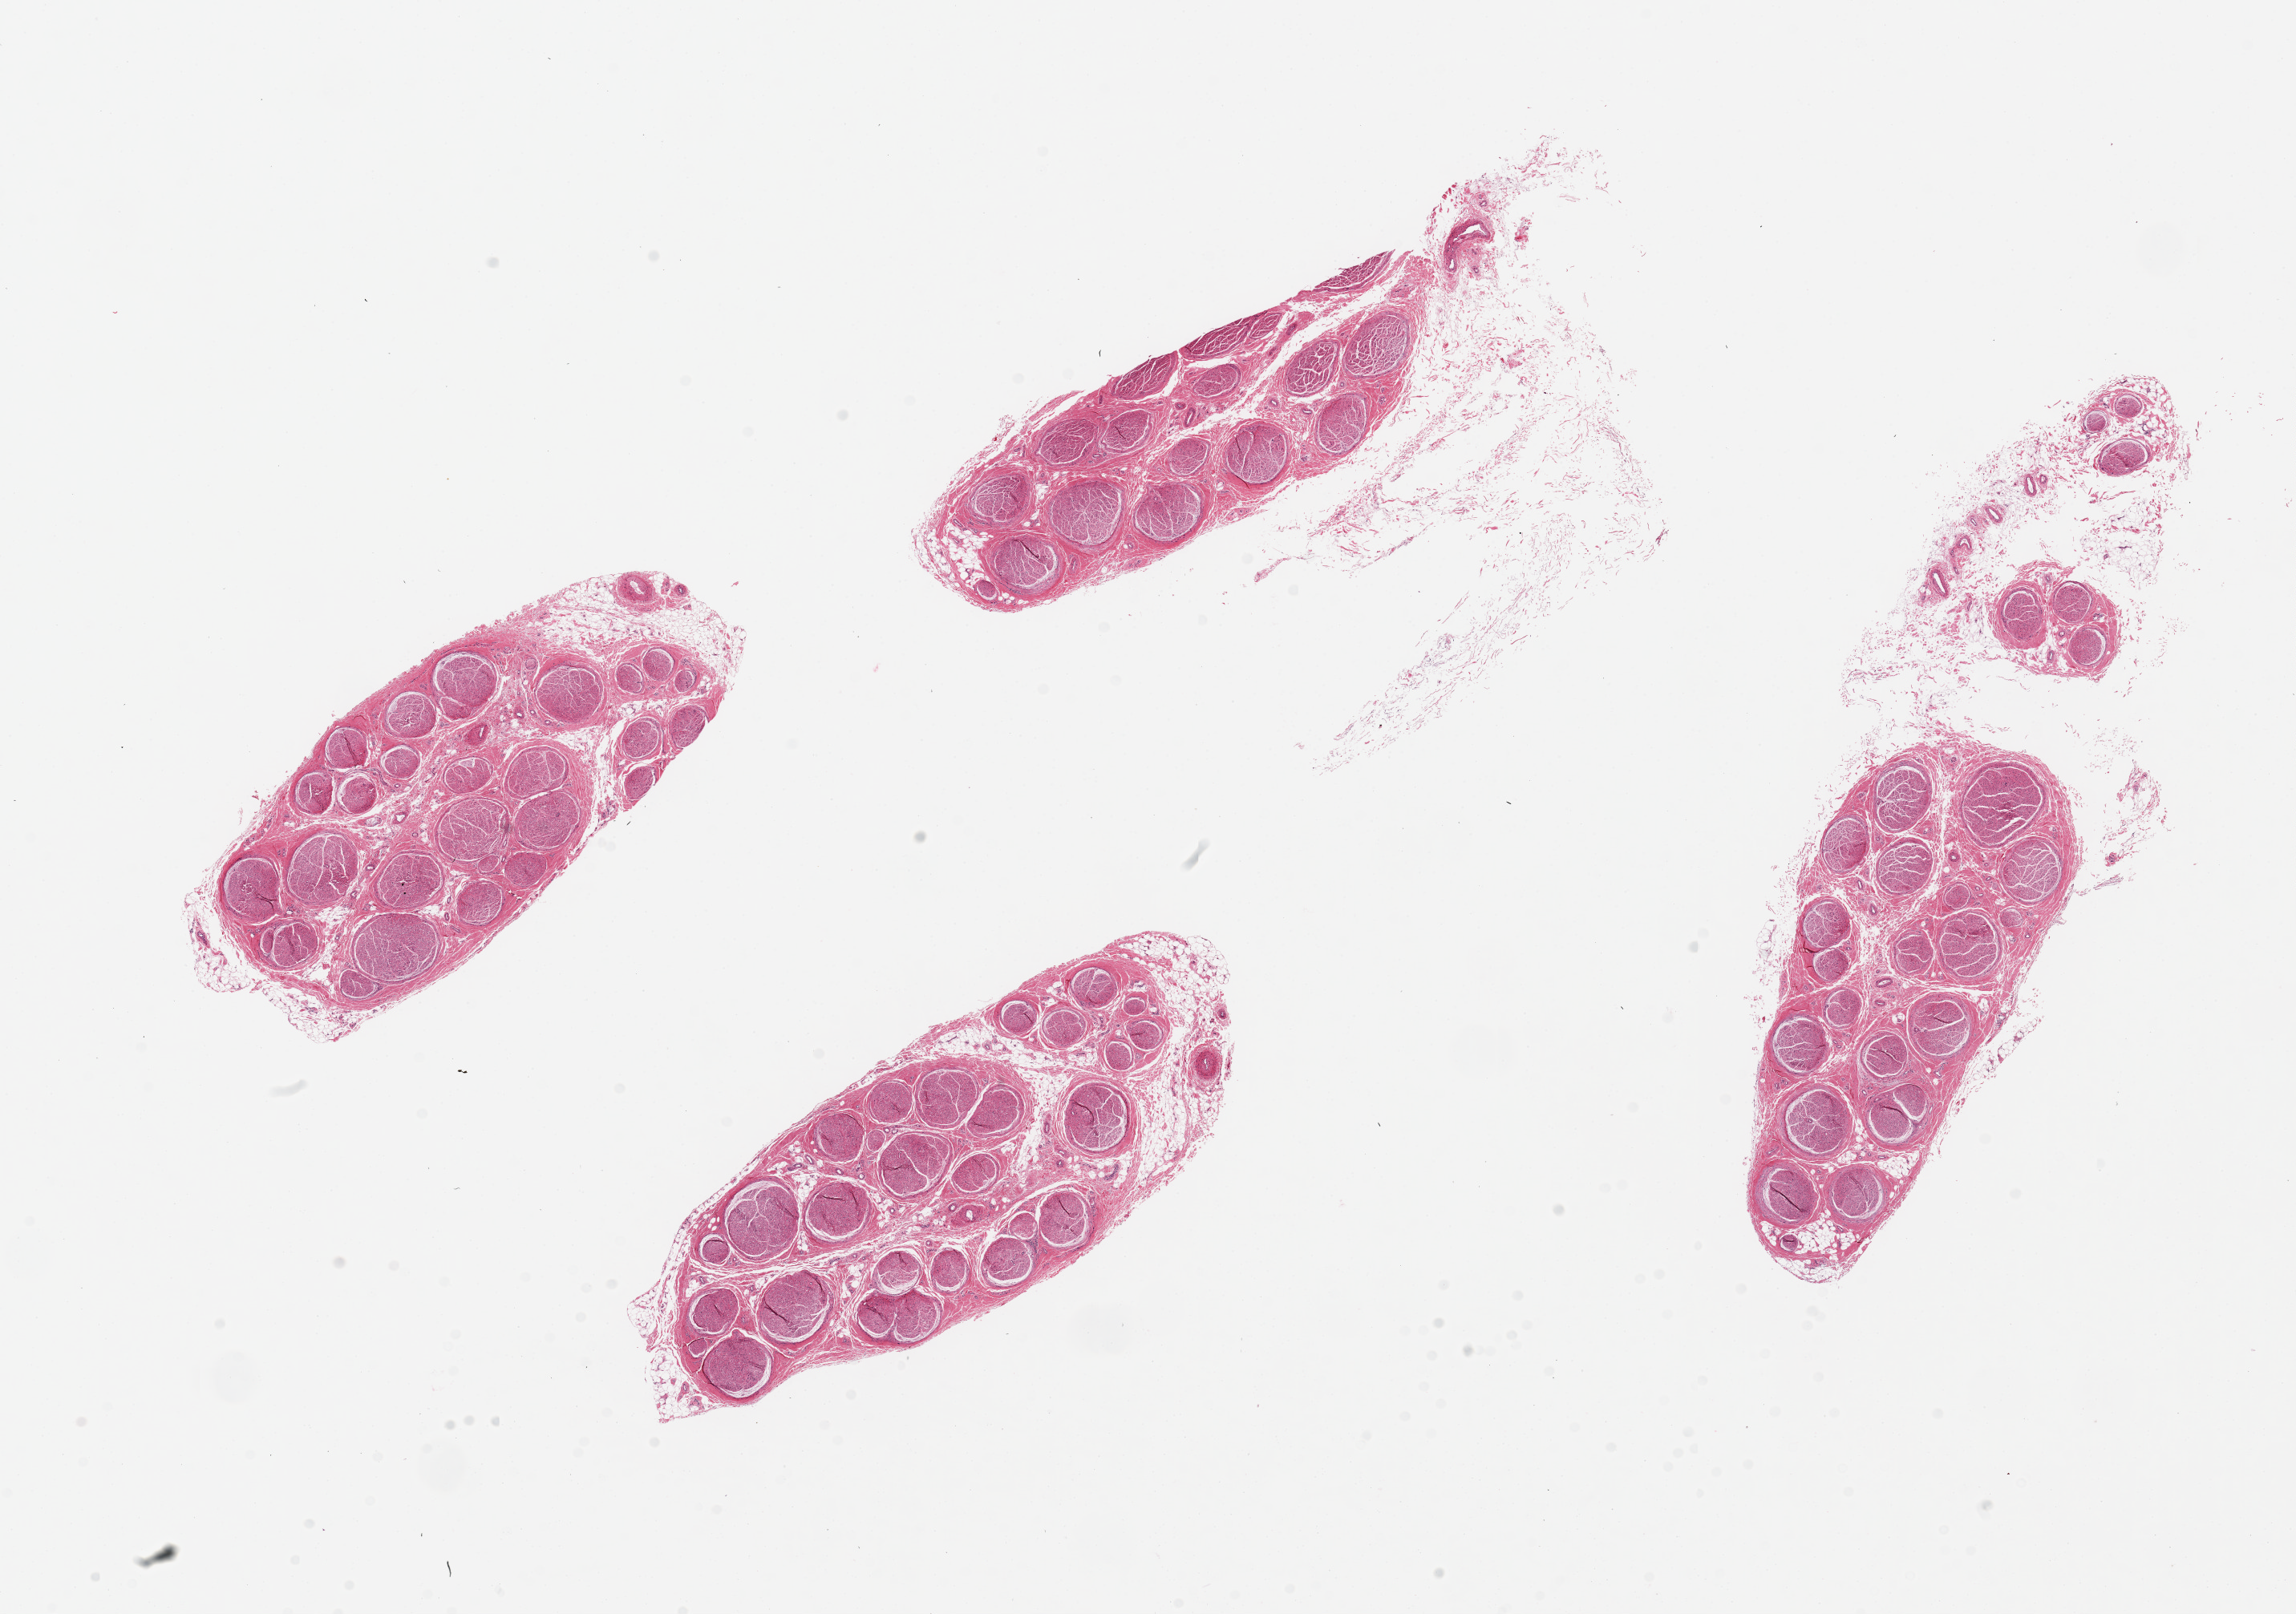
Haematoxylin and eosin whole-slide image — shown as a low-resolution overview of the whole scanned area (about 22.6 x 15.9 mm). PAXgene-fixed paraffin-embedded (PFPE) section. Target tissue: tibial nerve. Donor tissue sample. Donor: male.
Review note (as recorded): 4 pieces, up to 9x3.5mm; adherent nubbin of fat on 2, generally clean good specimens.